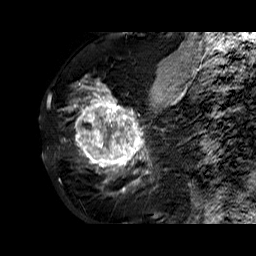
Breast MRI (dynamic contrast-enhanced), one sagittal slice; dynamic contrast-enhanced series, time point 2 of 6 at this slice position (early post-contrast); 1.5 T; TE 6.3 ms, TR 32.4 ms; 4 mm slice thickness; 256 × 256 image matrix, field of view 200 × 200 mm. Female patient. From the clinical record (not read from this slice): setting: breast cancer imaged before/during neoadjuvant chemotherapy; receptor status: HR-positive, HER2-negative.
Outlined on this slice (semi-automatically segmented with operator editing):
- analysis volume of interest (the breast-tissue region the enhancement analysis was run in; not a lesion): bounding box [x1, y1, x2, y2] px = [68, 72, 177, 183]
- tumour enhancement mask (voxels above the 100 % enhancement threshold inside the analysis volume of interest): [71, 84, 168, 183]